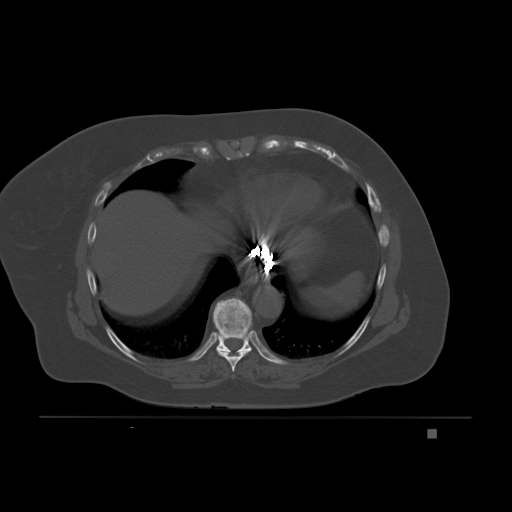
CT including the spine, one axial slice. Slice 114 of 221 in the series (ordered by position). Bone window (W 1800 / L 400 HU). 3 mm slice thickness. 512 × 512 image matrix, field of view 474 × 474 mm. Female patient, age 63 years. Case-level facts recorded for this patient, not image findings: primary cancer: breast.
Outlined on this slice (semi-automatically segmented with operator editing):
- T8 vertebra: bounding box [x1, y1, x2, y2] px = [216, 349, 249, 372]
- T9 vertebra: [213, 298, 252, 353]